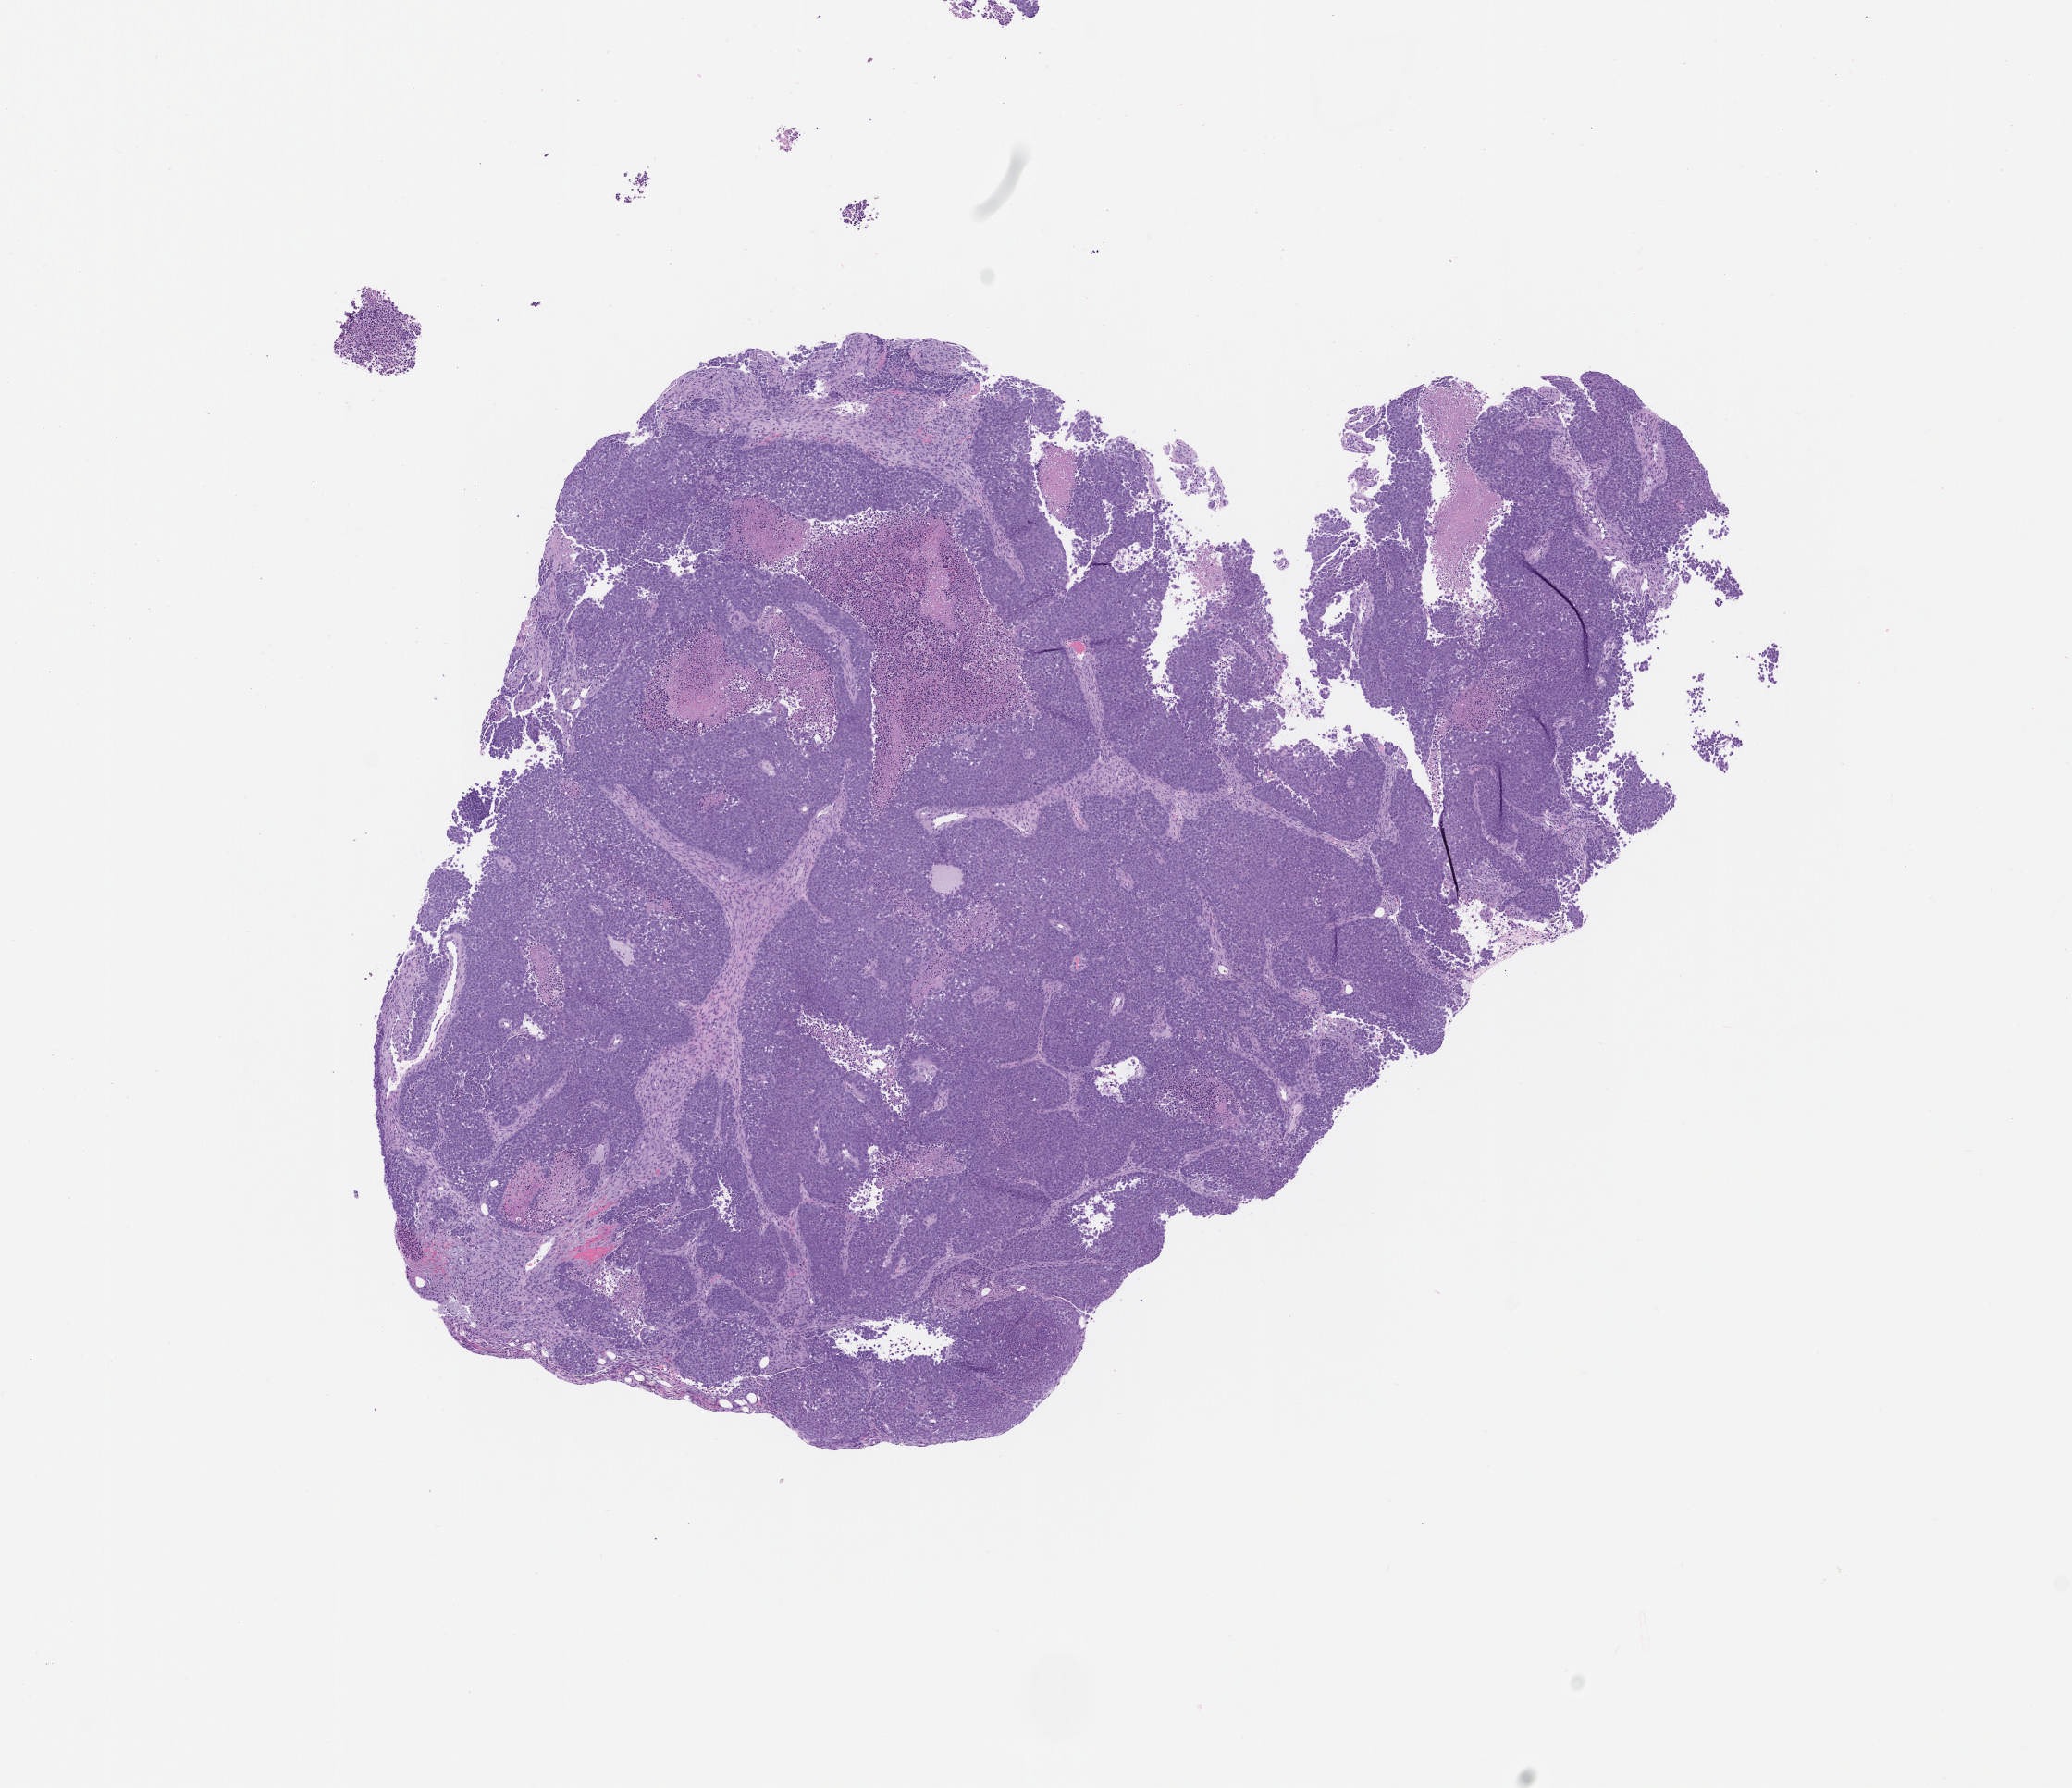
Hematoxylin and eosin (H&E) whole-slide image of a patient-derived xenograft (PDX) tumor grown in a mouse, passage 1 — whole scanned area (about 9.0 x 7.7 mm) shown as a low-resolution overview, formalin-fixed, paraffin-embedded (FFPE) tissue, originating tumor site category: lung.
Originating patient diagnosis: Lung Squamous Cell Carcinoma.